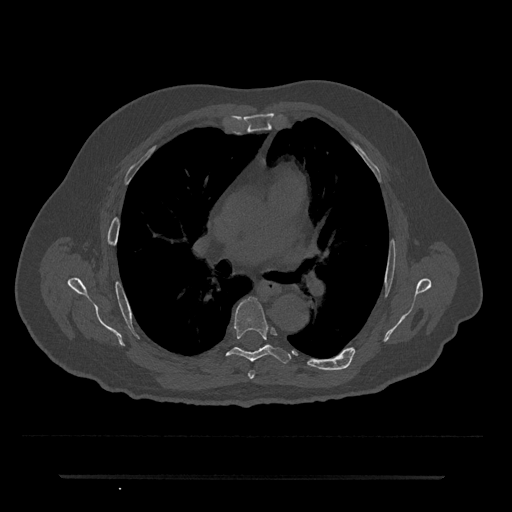
CT including the spine, one axial slice. Slice 438 of 797 in the series (ordered by position). Reconstruction kernel Br40s/3. 120 kVp. Bone window (W 1800 / L 400 HU). 0.5 mm slice thickness. 512 × 512 image matrix, field of view 437 × 437 mm. Patient: male, 69 years. Case-level facts recorded for this patient, not image findings: primary cancer: prostate.
Structures marked on this image (semi-automatically segmented with operator editing):
- T5 vertebra: bounding box [x1, y1, x2, y2] px = [248, 371, 255, 379]
- T6 vertebra: [227, 298, 291, 363]